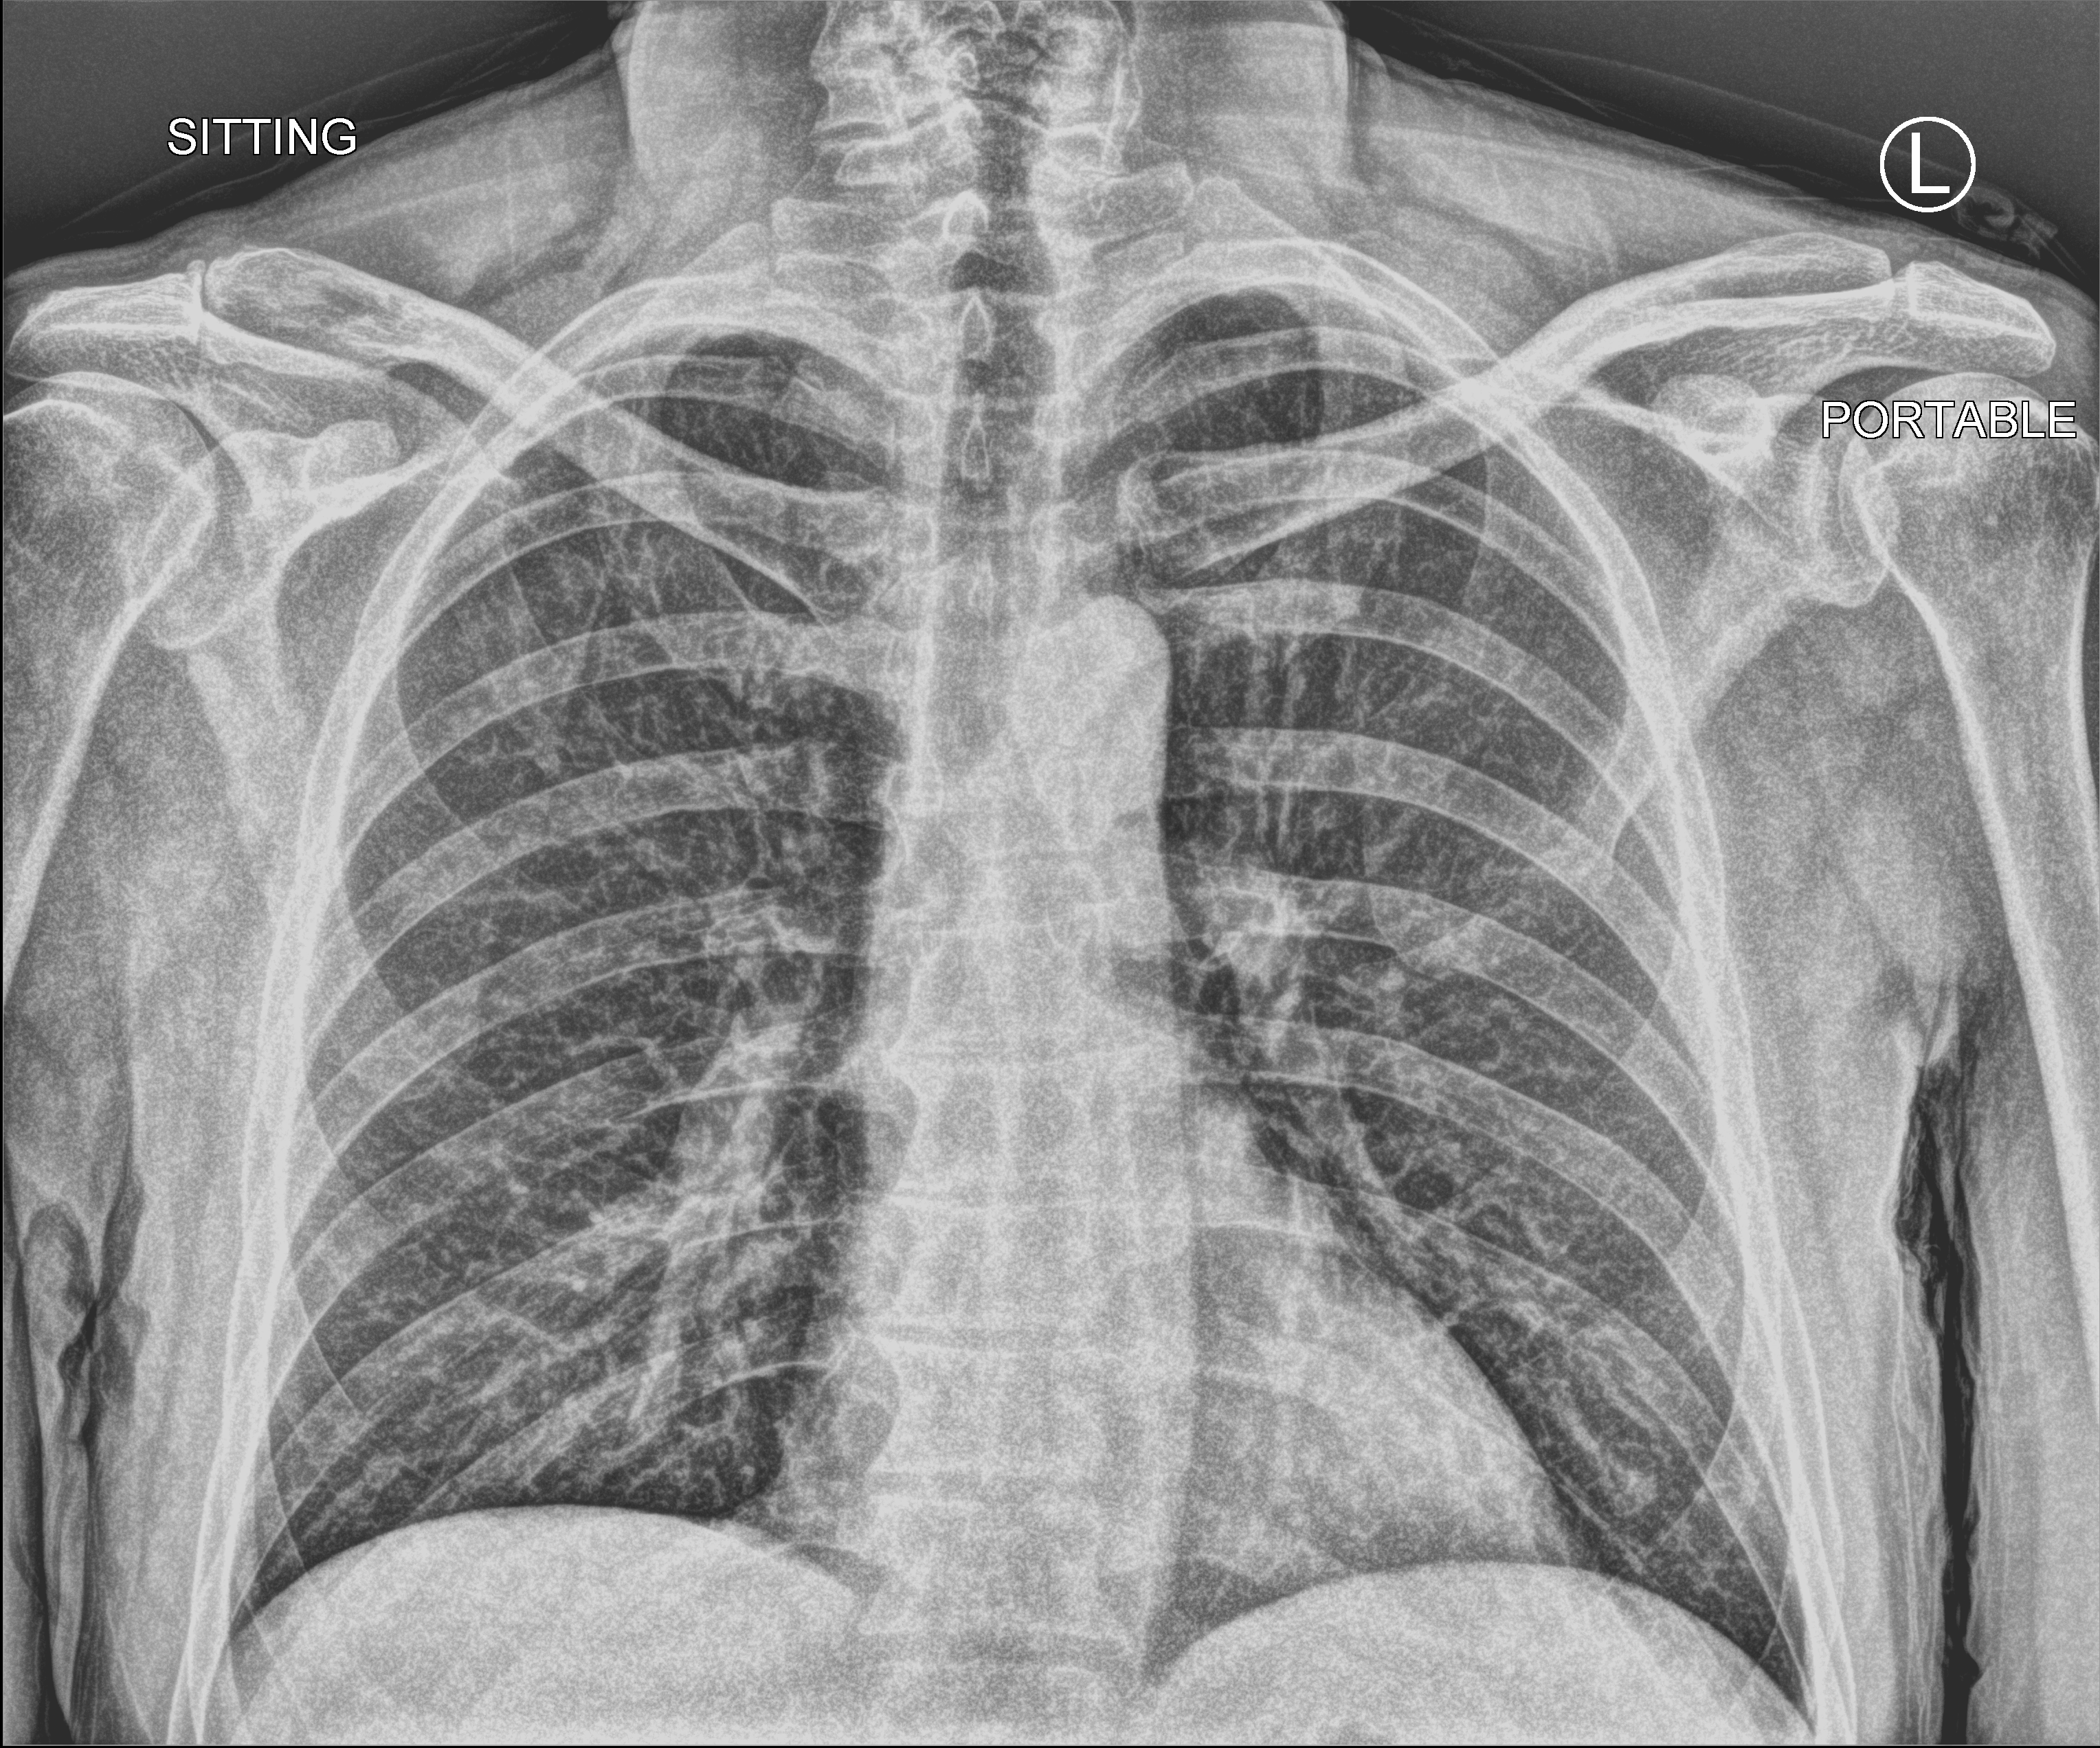
Portable chest radiograph, anteroposterior (AP) projection. Male patient hospitalised with COVID-19, age 18–59 years.
Admission-level facts for this patient (not findings on this image; timing relative to this image not recorded): admitted to intensive care during this hospital stay: no.